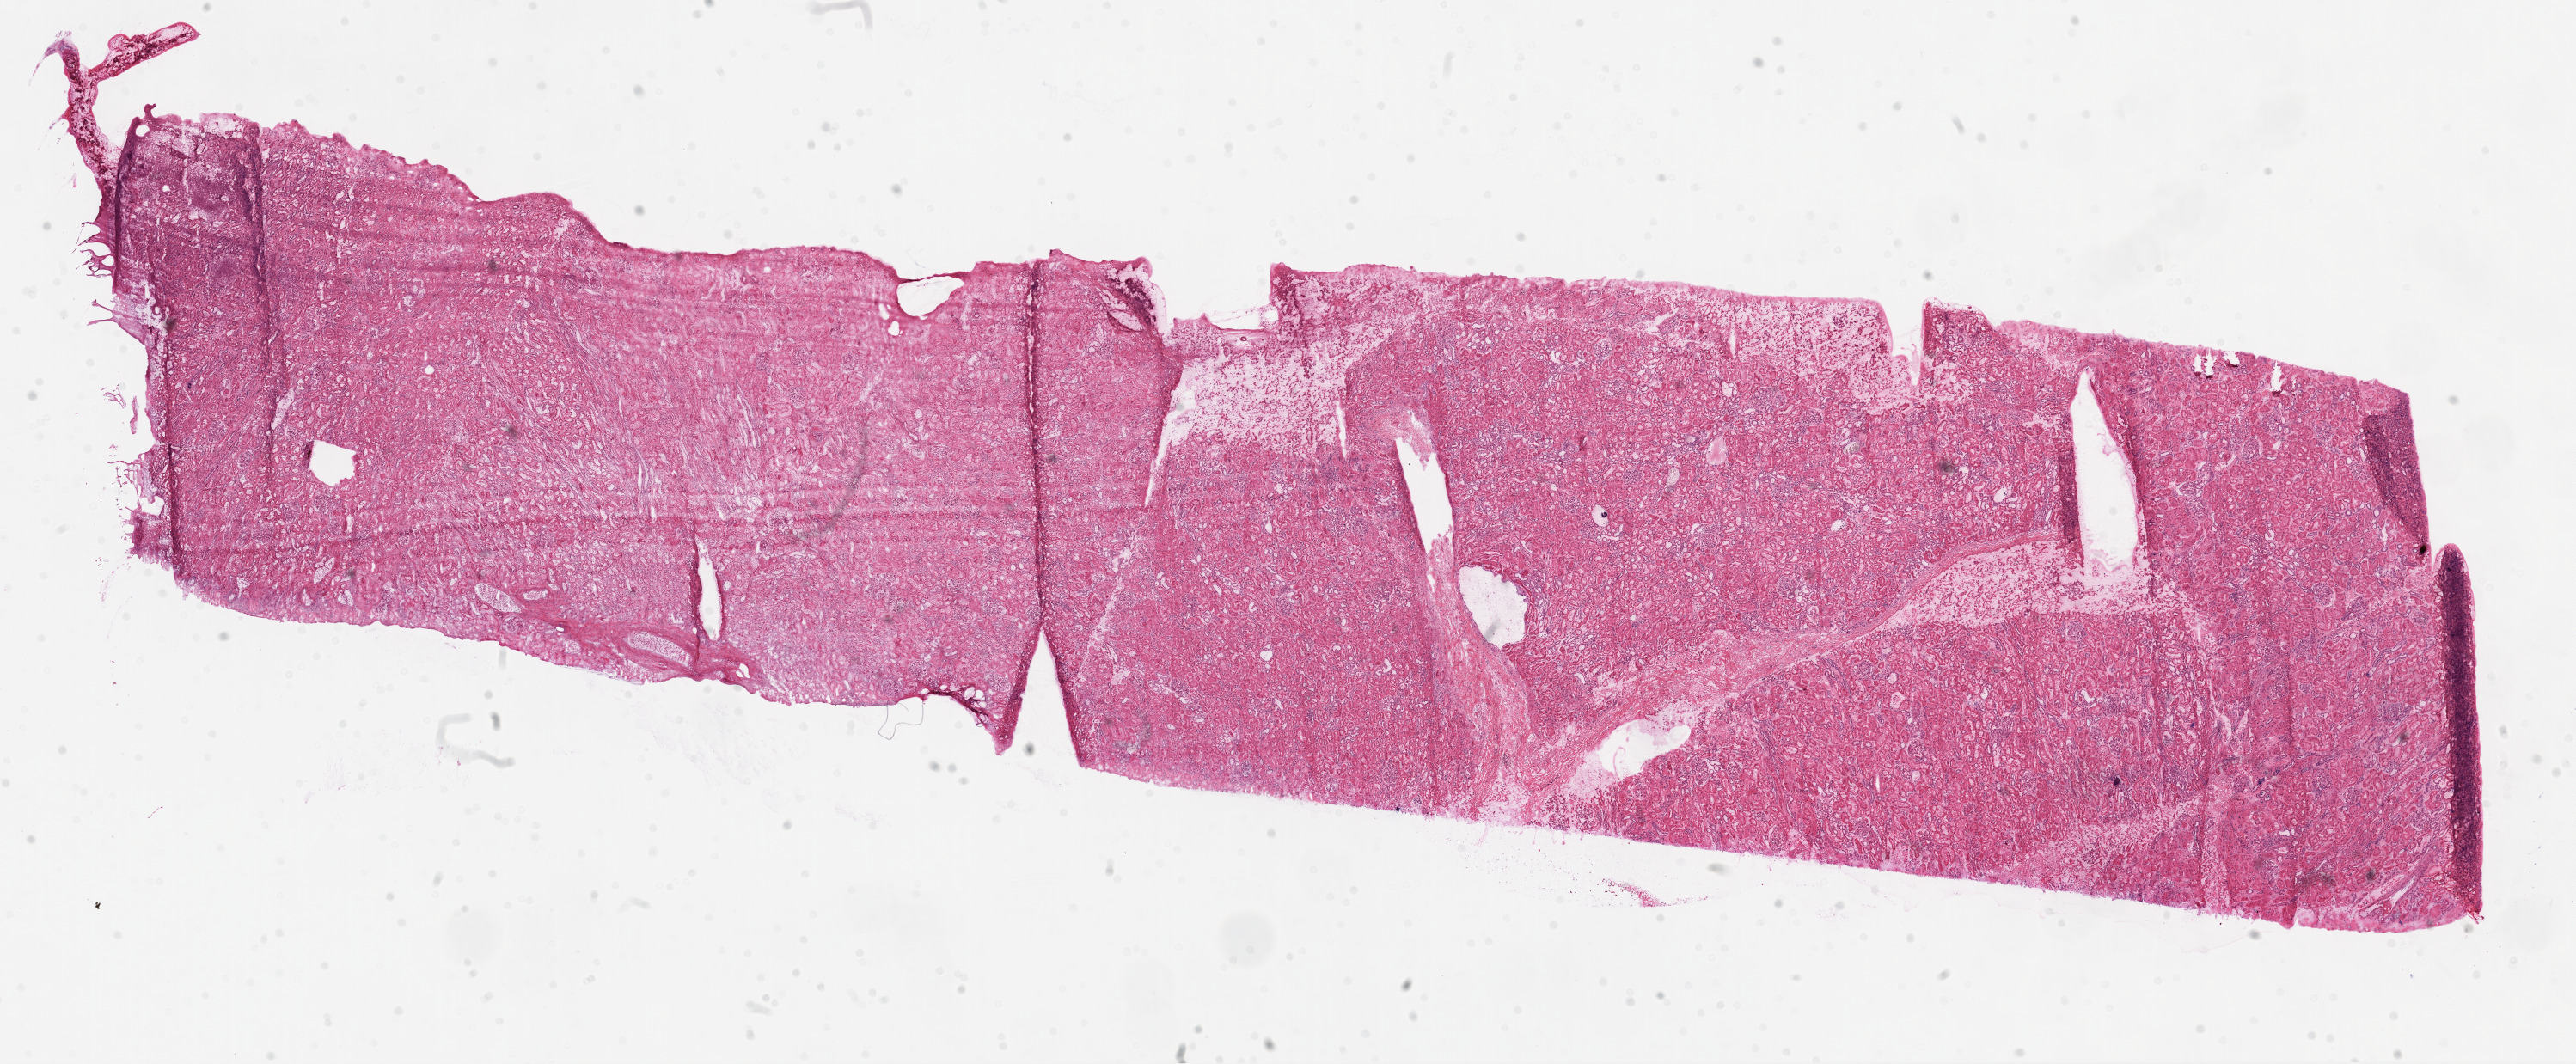
H&E whole-slide image — low-resolution overview of the scanned area, about 24.2 x 10.0 mm (from a 20x scan). Frozen section from the top of the tissue portion. Sample: solid tissue normal (non-tumour tissue), kidney. Patient: female, age at initial diagnosis 44 years.
* this section: solid tissue normal sample (biorepository sample class)
* patient diagnosis: Clear cell adenocarcinoma, NOS